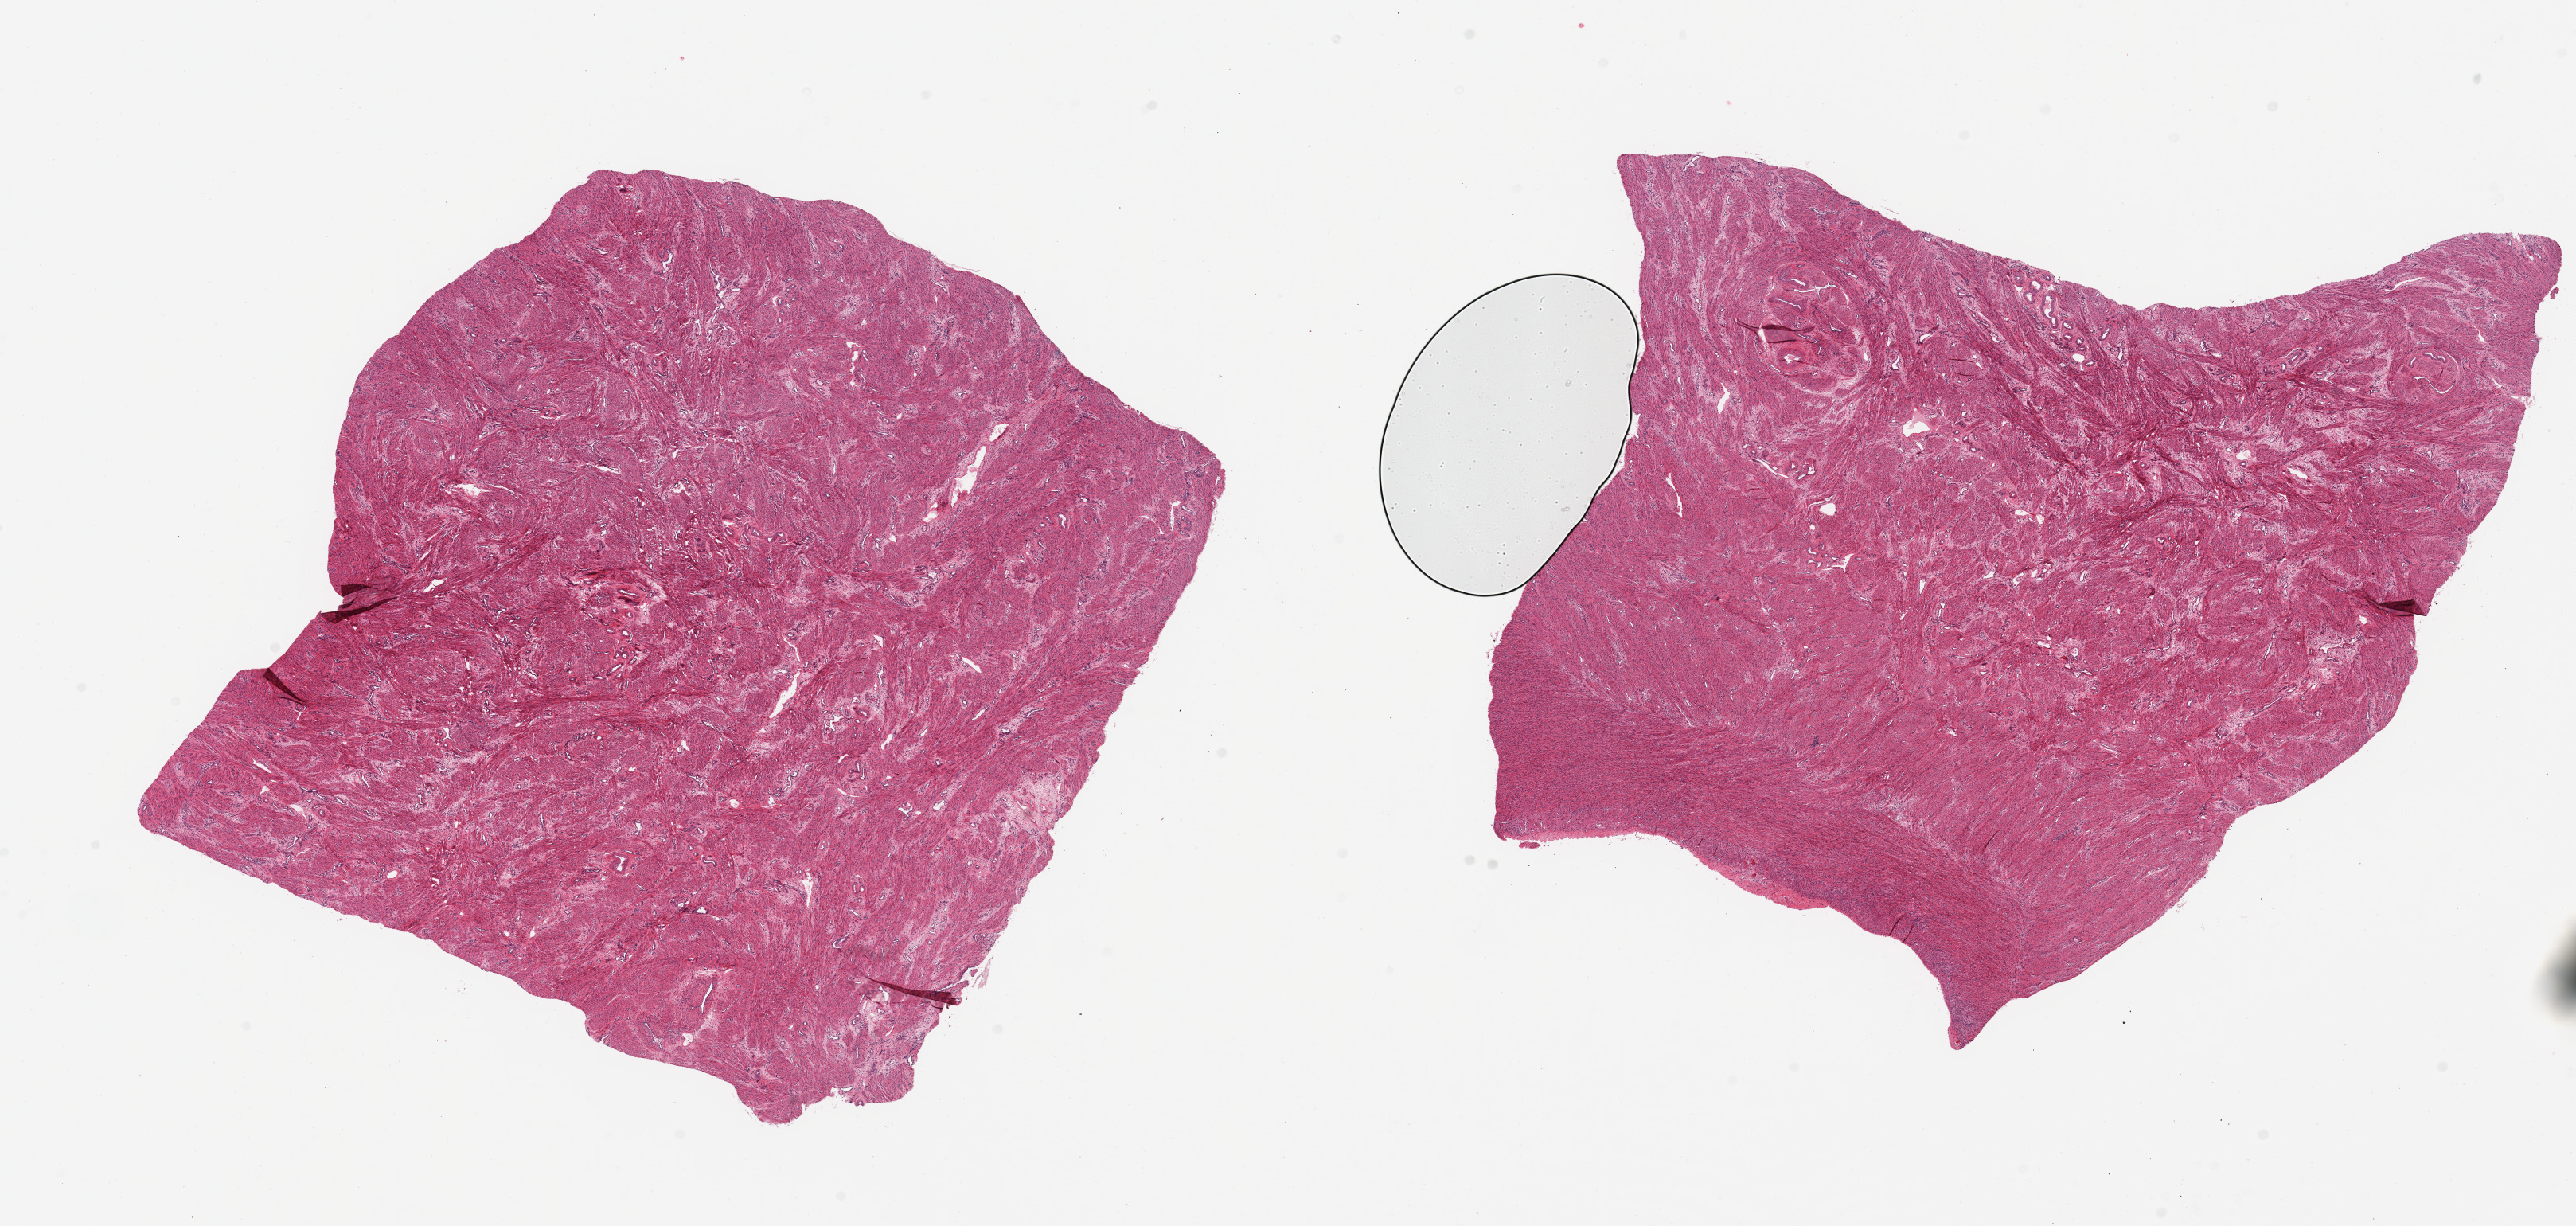
Digitized haematoxylin and eosin-stained section, brightfield — low-resolution overview of the scanned area, about 25.6 x 12.2 mm (acquisition: 20x scan), PAXgene-fixed, paraffin-embedded tissue, target tissue: uterus, tissue donor sample. Female donor.
Reviewer comment on this tissue sample: 2 pieces; only myometrium in these sections.